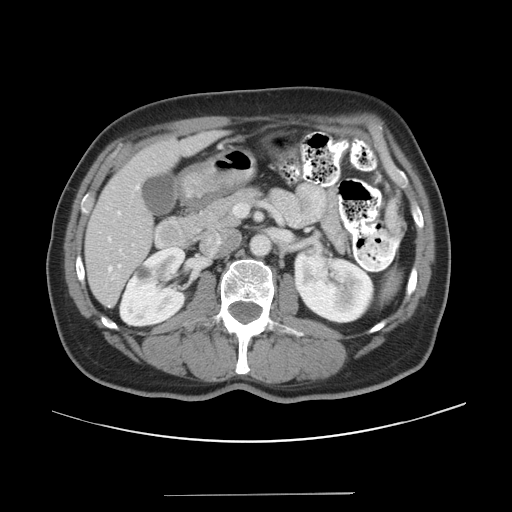
Contrast-enhanced abdominal CT, one axial slice; slice 16 of 43 in the series (ordered by position); reconstruction kernel STANDARD; intravenous contrast given; soft-tissue window (W 400 / L 40 HU); 5 mm slice thickness; 512 × 512 image matrix. Male patient, age 65 years. From the clinical record (not read from this slice): diagnosis: colorectal cancer liver metastases, imaged before liver resection; multiple liver metastases: no; largest metastasis: 3.8 cm.
Outlined on this slice (outlined manually by an expert reader):
- hepatic veins: box from (x=108, y=238) to (x=121, y=271) px
- liver: (x=86, y=133)–(x=219, y=305)
- planned liver remnant (the part of the liver to remain after resection): (x=86, y=133)–(x=219, y=305)